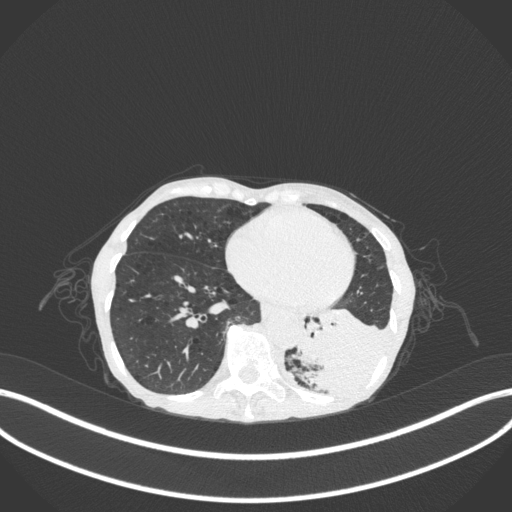
Chest CT, one axial slice. Slice 81 of 347 in the series (ordered by position). Reconstruction kernel B31f. 120 kVp. Lung window (W 1500 / L -600 HU). 1 mm slice thickness. 512 × 512 image matrix, field of view 400 × 400 mm. Female patient, age 70 years. Case-level facts recorded for this patient, not image findings: clinical TNM (as recorded): T3 N0 M0; histopathological grade: G3.
Outlined on this slice (bounding box drawn by a radiologist):
- lung tumour (recorded histology: small cell carcinoma): bounding box (x1, y1, x2, y2) in pixels: (289, 304, 394, 401)